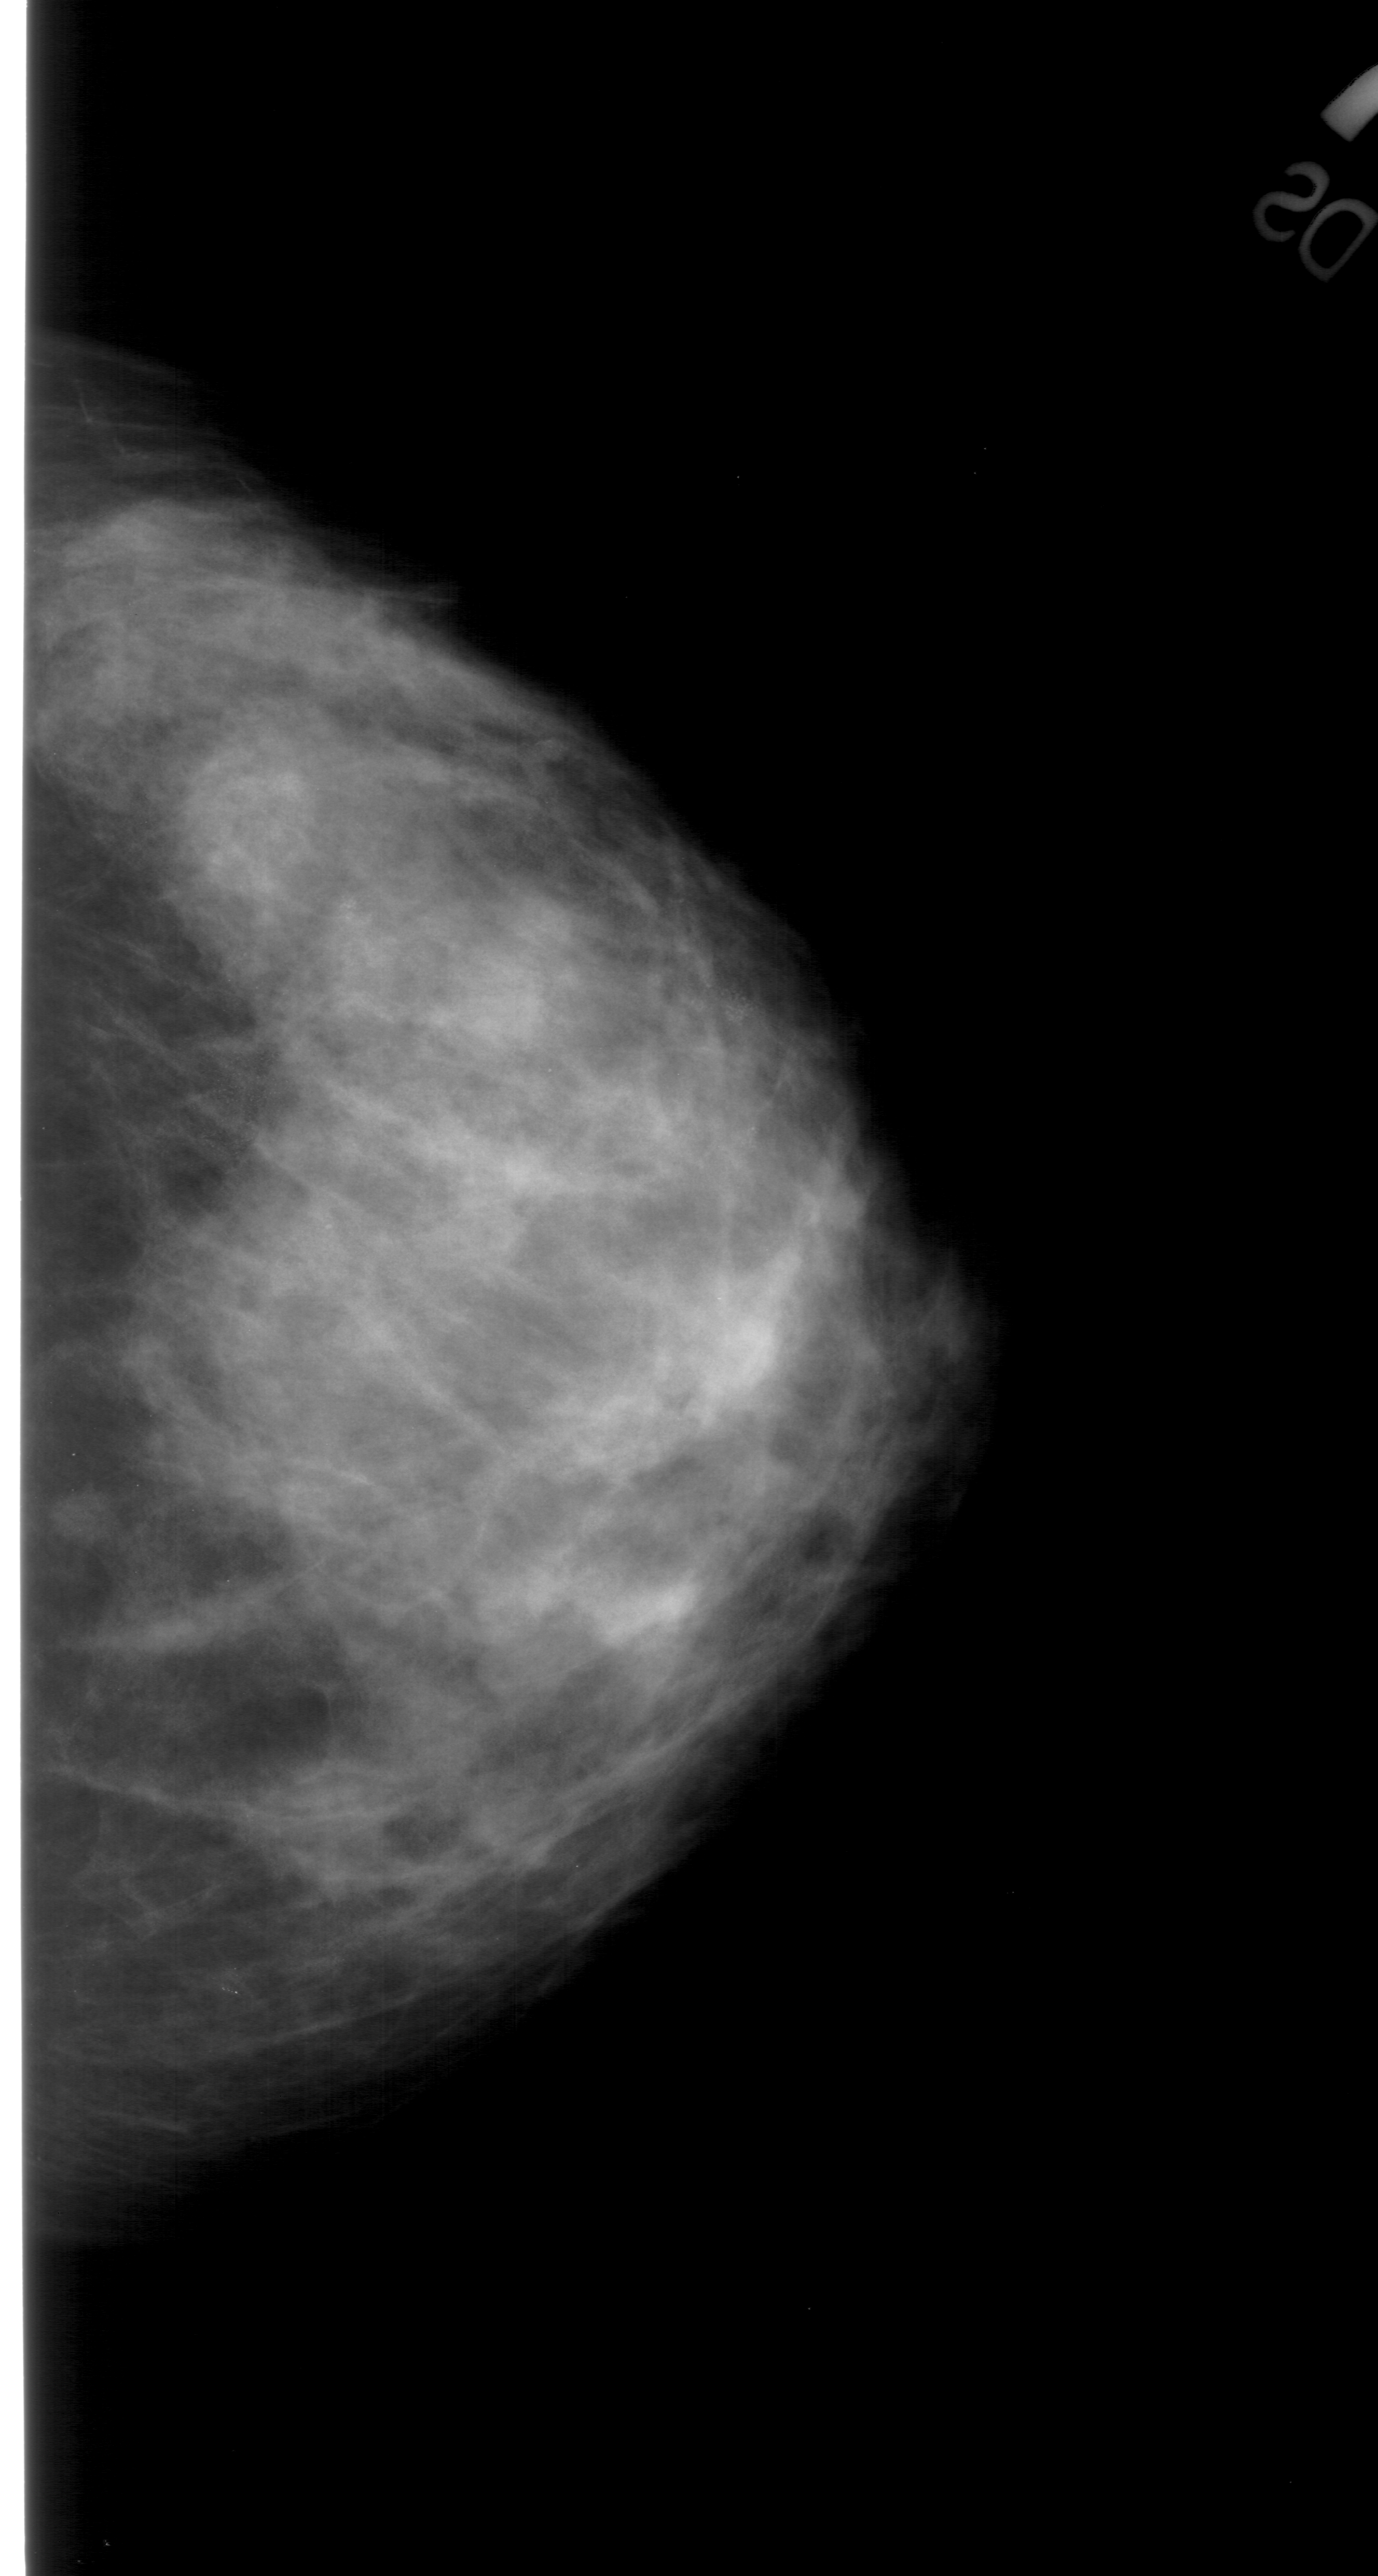
Digitized screen-film mammogram; right breast; CC view; BI-RADS breast density category 4 (scale 1–4).
Radiologist-marked abnormalities on this image: calcifications, morphology pleomorphic, distribution segmental; BI-RADS assessment category 4; pathology result (as recorded, not read from the image): malignant.